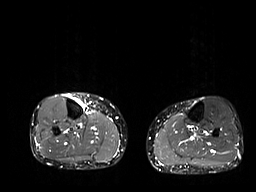
MRI of an extremity soft-tissue mass, one axial slice; slice 10 of 32 in the series (ordered by position); STIR; 6 mm slice thickness; 256 × 192 image matrix, field of view 375 × 281 mm. Female patient. Case-level facts recorded for this patient, not image findings: histological type: undifferentiated – high grade; grade: high; site of the primary tumour: right thigh.
Structures marked on this image (manually delineated by an expert):
- gross tumour volume (mass): bounding box [x1, y1, x2, y2] px = [74, 99, 84, 107]